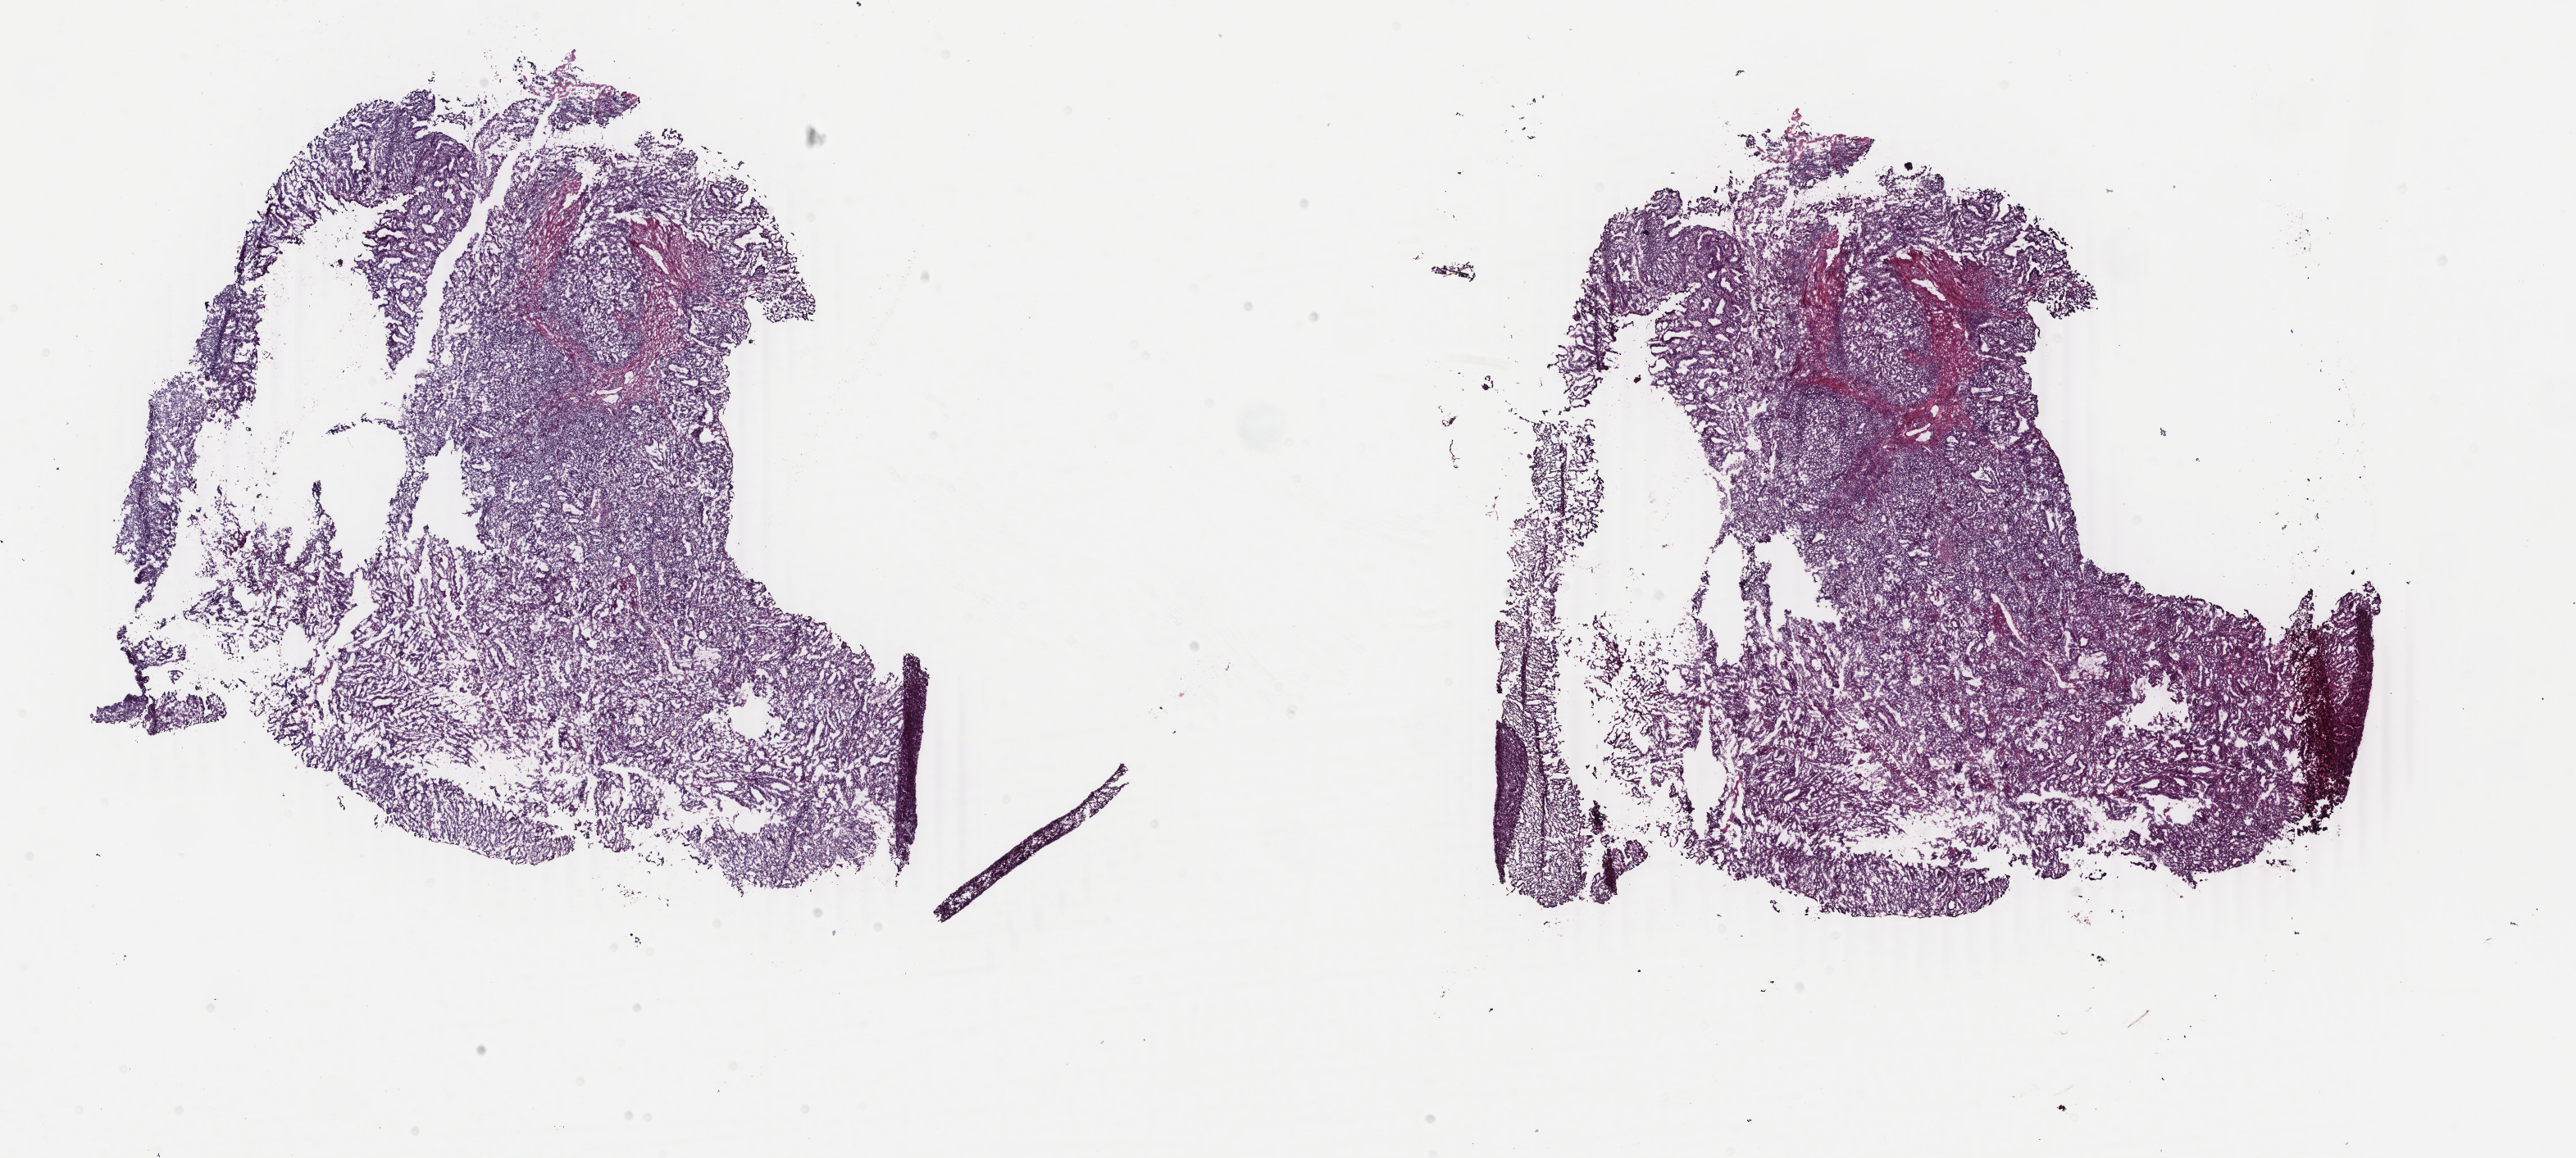
Hematoxylin and eosin (H&E) stained whole-slide image — shown as a low-resolution overview of the whole scanned area (about 25.0 x 11.2 mm, slide scanned at 40x); frozen section from the top of the tissue portion; uterus, primary tumour sample. Female patient; age at initial diagnosis 58 years. Histologic grade: G1 (well differentiated). Pathologist review of this section (percent, as recorded): tumour cells 70%, tumour nuclei 70%, normal cells 0%, stromal cells 25%, necrosis 5%. Infiltration values recorded for this section: lymphocyte infiltration 40%, monocyte infiltration 20%, neutrophil infiltration 30%.
• diagnosis: Endometrioid adenocarcinoma, NOS
• FIGO stage: IIIA